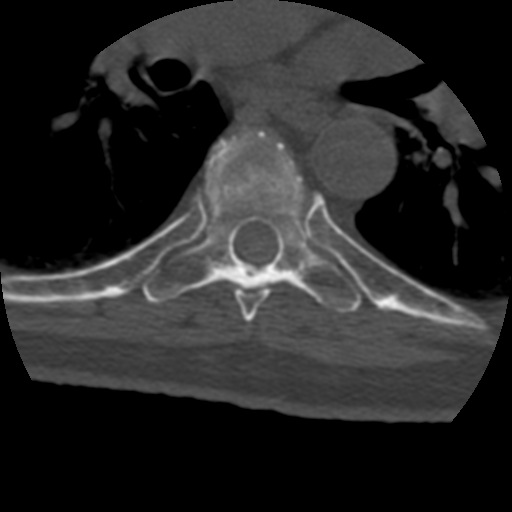
CT including the spine, one axial slice; position 289 of 399 along the scan axis; reconstruction kernel STANDARD; bone window (W 1800 / L 400 HU); 1.25 mm slice thickness; 512 × 512 image matrix, field of view 160 × 160 mm. Patient age 69 years. Case-level facts recorded for this patient, not image findings: primary cancer: prostate.
Outlined on this slice (semi-automatically segmented with operator editing):
- T6 vertebra: box from (x=231, y=136) to (x=282, y=321) px
- T7 vertebra: (x=143, y=130)–(x=362, y=313)